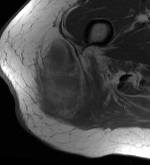
MRI of an extremity soft-tissue mass, one axial slice. Slice 16 of 56 in the series (ordered by position). MR volume resampled by the dataset authors to the PET/CT grid (not the native acquisition matrix). 150 × 165 image matrix, field of view 146 × 161 mm. Female patient. From the clinical record (not read from this slice): histological type: epithelioid sarcoma with vascular differentiation; site of the primary tumour: right buttock.
Outlined on this slice (expert contour drawn on MRI and transferred to this co-registered scan by the dataset authors):
- gross tumour volume (mass): bounding box <32,40,106,123> (left, top, right, bottom; pixels)